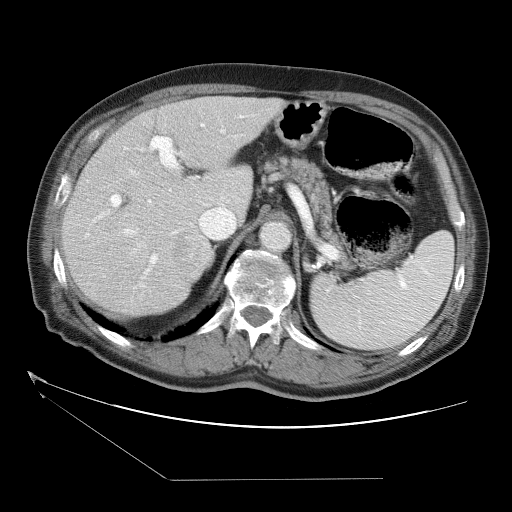
Contrast-enhanced abdominal CT (liver protocol), one axial slice; slice 22 of 38 in the series (ordered by position); reconstruction kernel STANDARD; 120 kVp; one of 2 acquisitions stored at this slice position; soft-tissue window (W 400 / L 40 HU); 512 × 512 image matrix. From the clinical record (not read from this slice): diagnosis: hepatocellular carcinoma (patient treated with transarterial chemoembolisation; whether this scan precedes or follows treatment is not stated here); TNM stage (as recorded): Stage-II; Child-Pugh class: A; tumour size: 0.8 cm.
Structures marked on this image (semi-automatic segmentation, software-assisted and operator-edited):
- abdominal aorta: bounding box <261,222,290,250> (left, top, right, bottom; pixels)
- liver parenchyma outside the tumour (the mass and vessels are separate outlines, so this box may not span the whole liver): <62,96,285,316>
- mass: <173,229,215,283>
- liver vessels: <84,116,242,304>